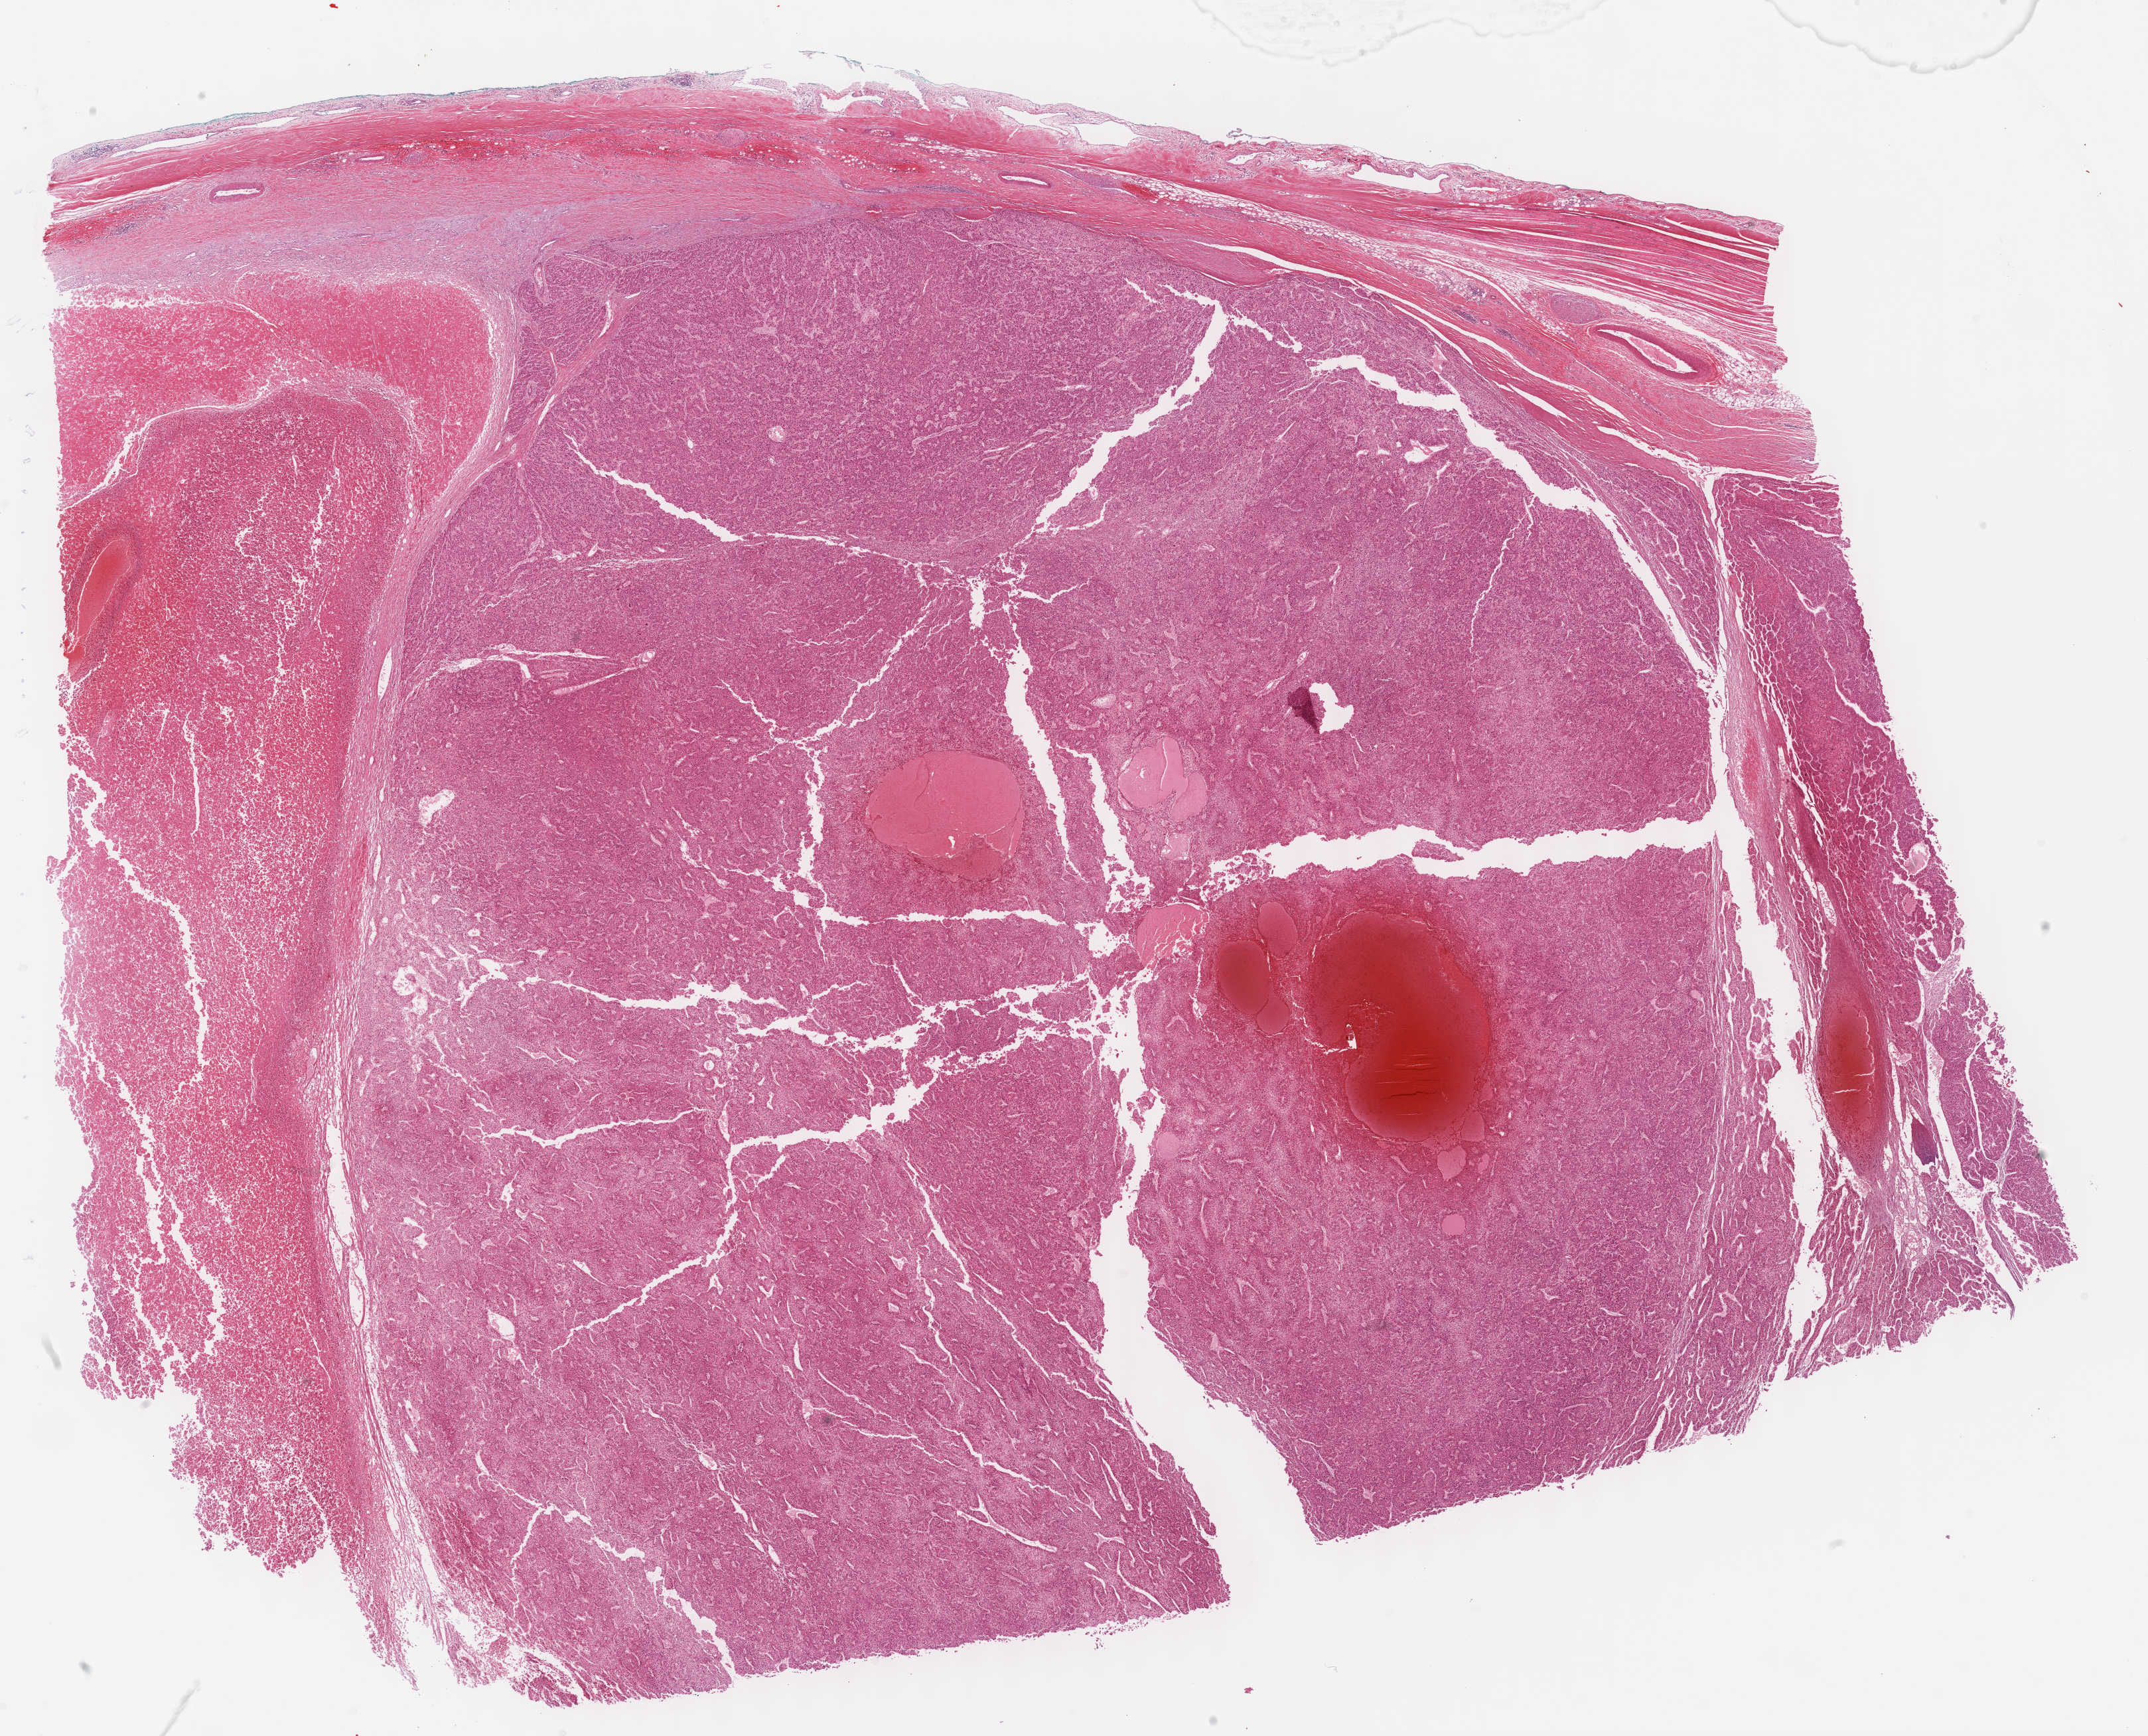
Whole-slide histology image, H&E, whole scanned area (about 26.2 x 21.1 mm, acquisition: 40x scan) shown as a low-resolution overview. Formalin-fixed paraffin-embedded (FFPE) diagnostic section. Liver, primary tumour sample. Patient: male, age at initial diagnosis 66 years. Histologic grade: G3 (poorly differentiated).
TNM: T3a N0 M0. AJCC pathologic stage: IIIA (7th edition). Histologic diagnosis: Hepatocellular carcinoma, NOS.